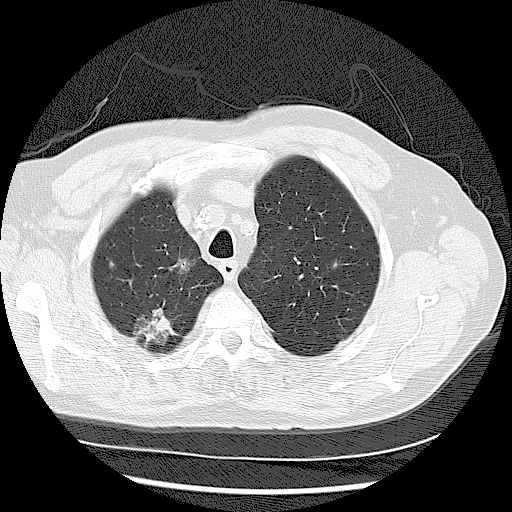
Low-dose screening chest CT, one axial slice. Position 96 of 122 along the scan axis. Reconstruction kernel LUNG. Lung window (W 1500 / L -600 HU). 2.5 mm slice thickness. 512 × 512 image matrix.
Outlined on this slice (outlined manually by an expert reader):
- lesion 1 (tumor, upper lobe of right lung): box from (x=133, y=309) to (x=176, y=345) px